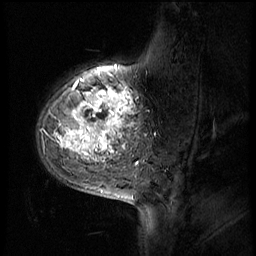
Breast MRI (dynamic contrast-enhanced), one sagittal slice. Slice 14 of 56 in the series (ordered by position). 4 images stored at this slice position (order not interpretable as contrast timing). 1.5 T. TE 4.2 ms, TR 8.9 ms. 256 × 256 image matrix, field of view 220 × 220 mm. Patient: female, 51 years. From the clinical record (not read from this slice): setting: breast cancer imaged before/during neoadjuvant chemotherapy; receptor status: triple-negative.
Outlined on this slice (semi-automatic segmentation, software-assisted and operator-edited):
- analysis volume of interest (the breast-tissue region the enhancement analysis was run in; not a lesion): box from (x=37, y=70) to (x=150, y=173) px
- tumour enhancement mask (voxels above the 140 % enhancement threshold inside the analysis volume of interest): (x=57, y=78)–(x=134, y=159)